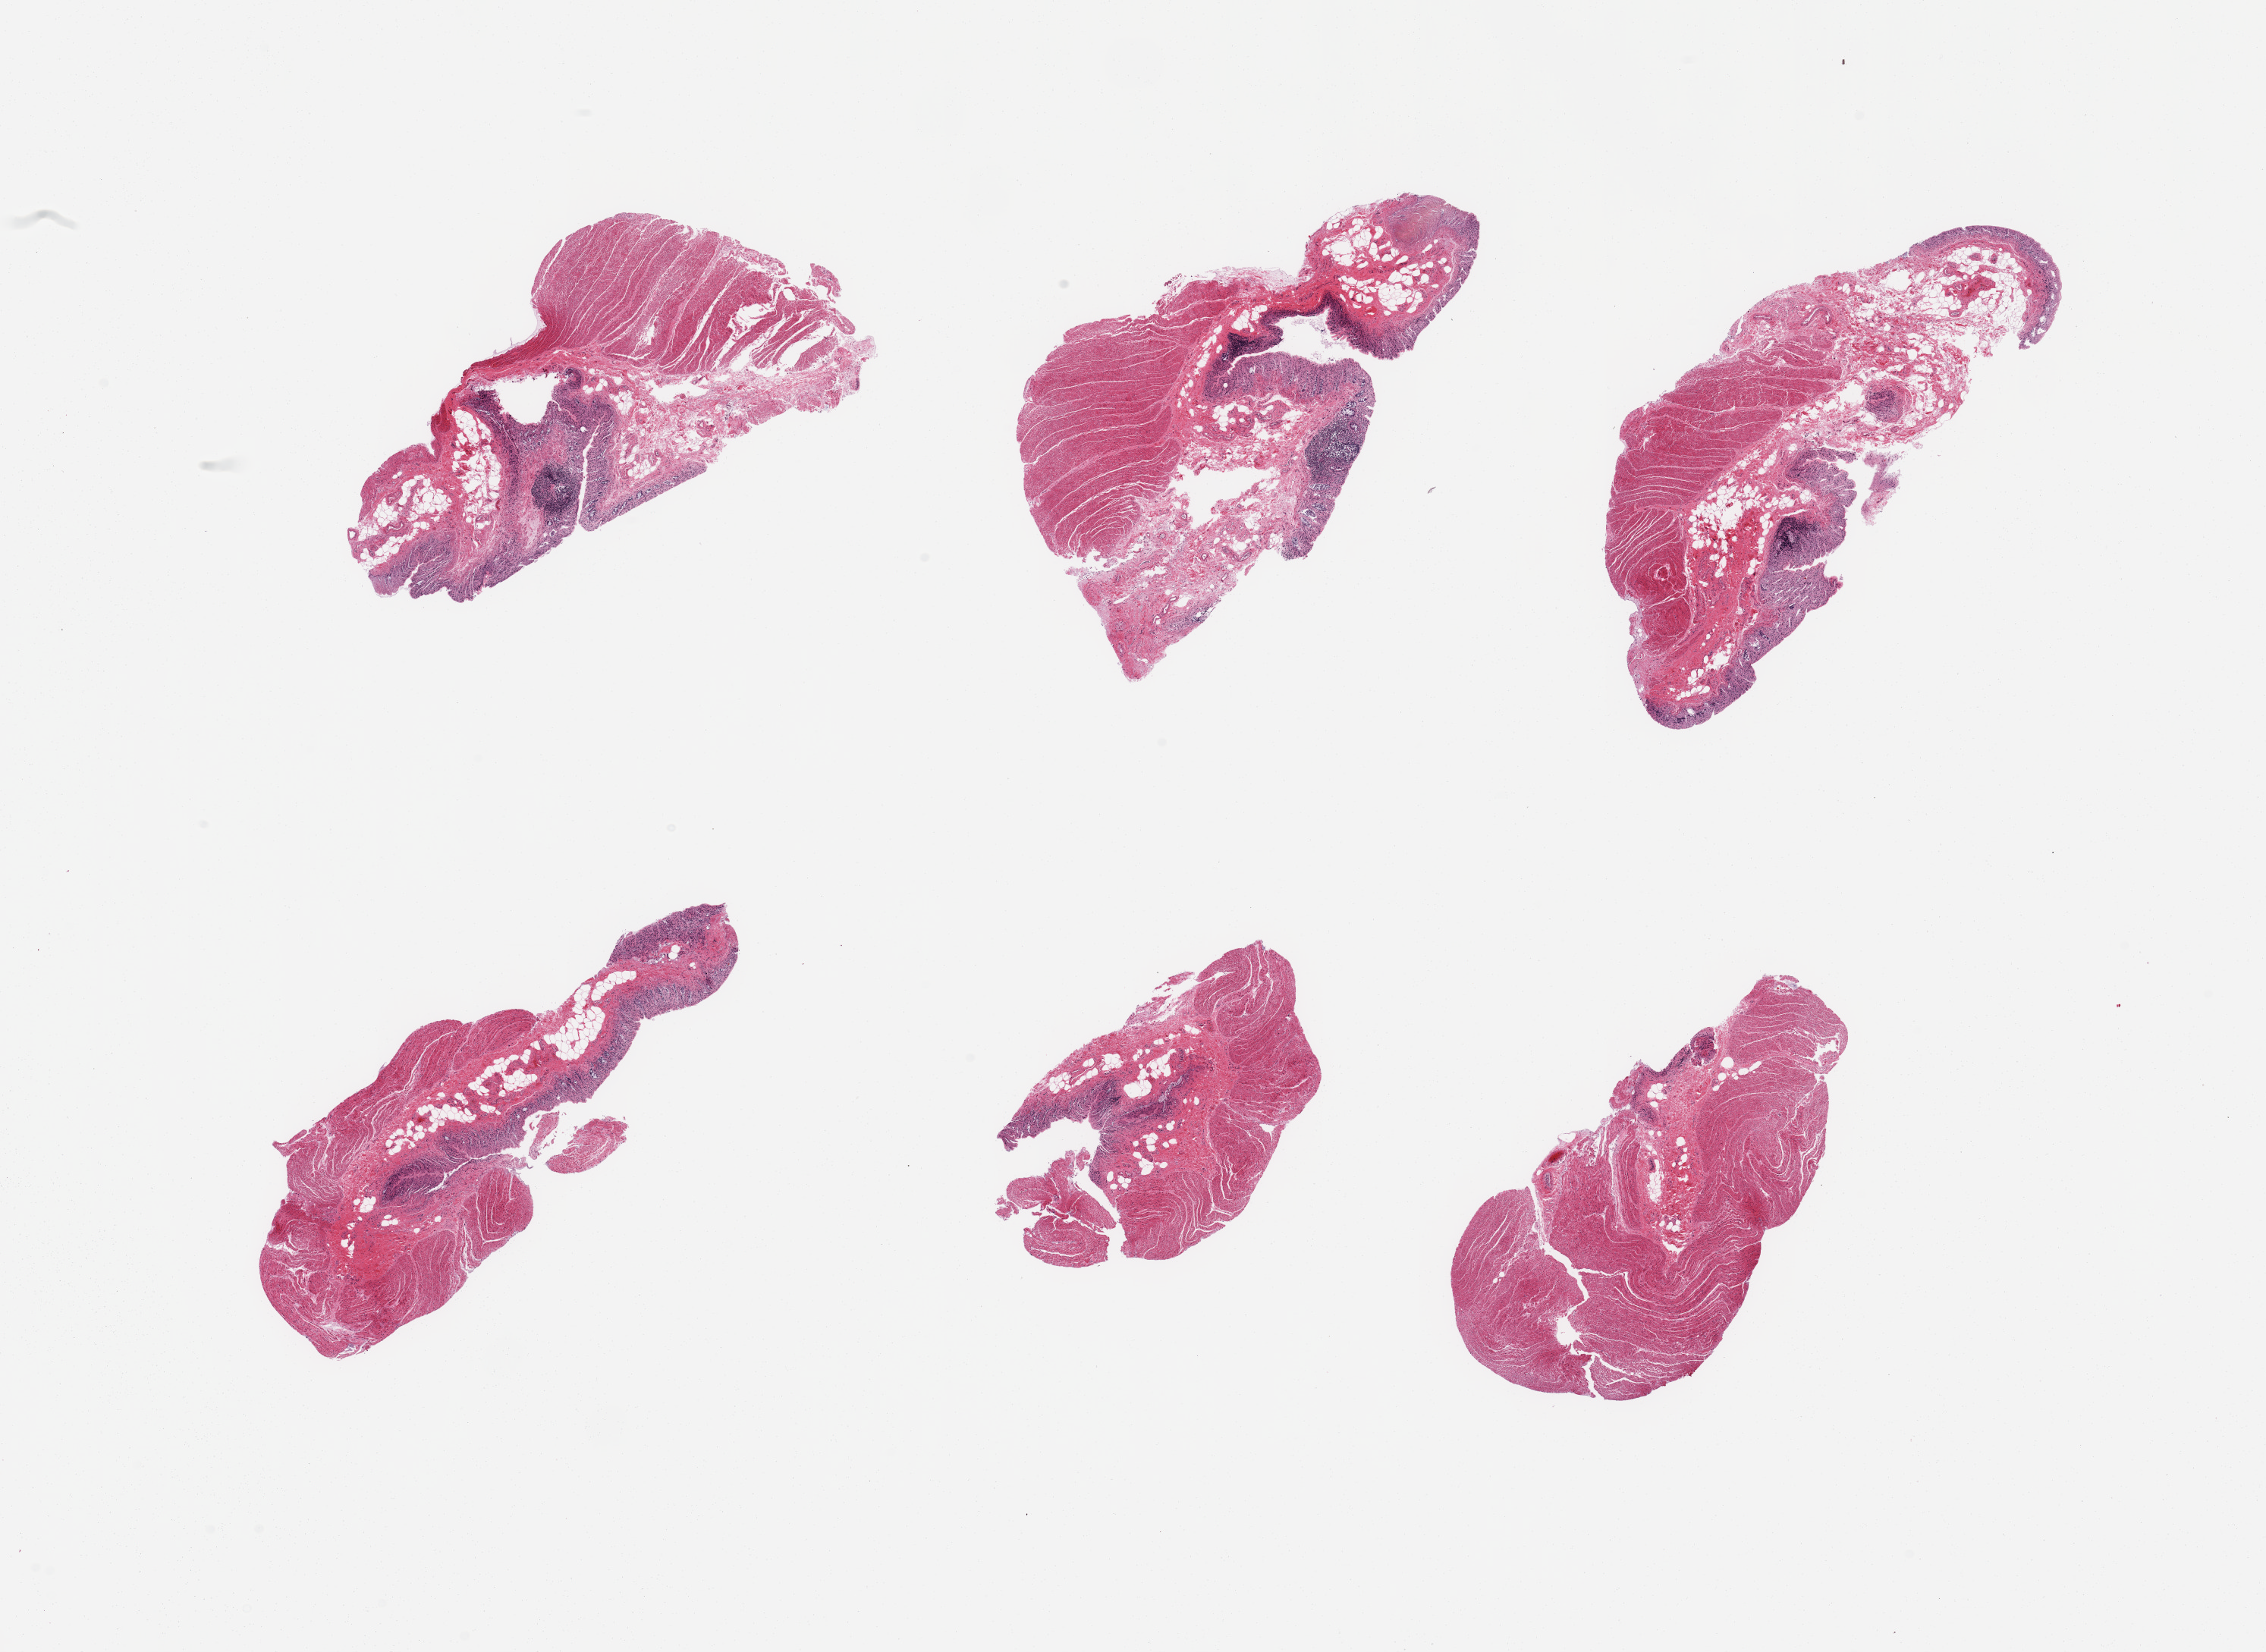
Whole-slide image, hematoxylin and eosin (H&E) stain — a low-resolution overview of the entire scanned area, about 23.6 x 17.2 mm; PAXgene-fixed paraffin-embedded (PFPE) section; sampled site (target tissue): sigmoid colon; donor tissue sample.
Review note (as recorded): 6 pieces; 5 of 6 contain autolyzed mucosa and abundant submucosa; muscularis propria comprises 30 to 80%.